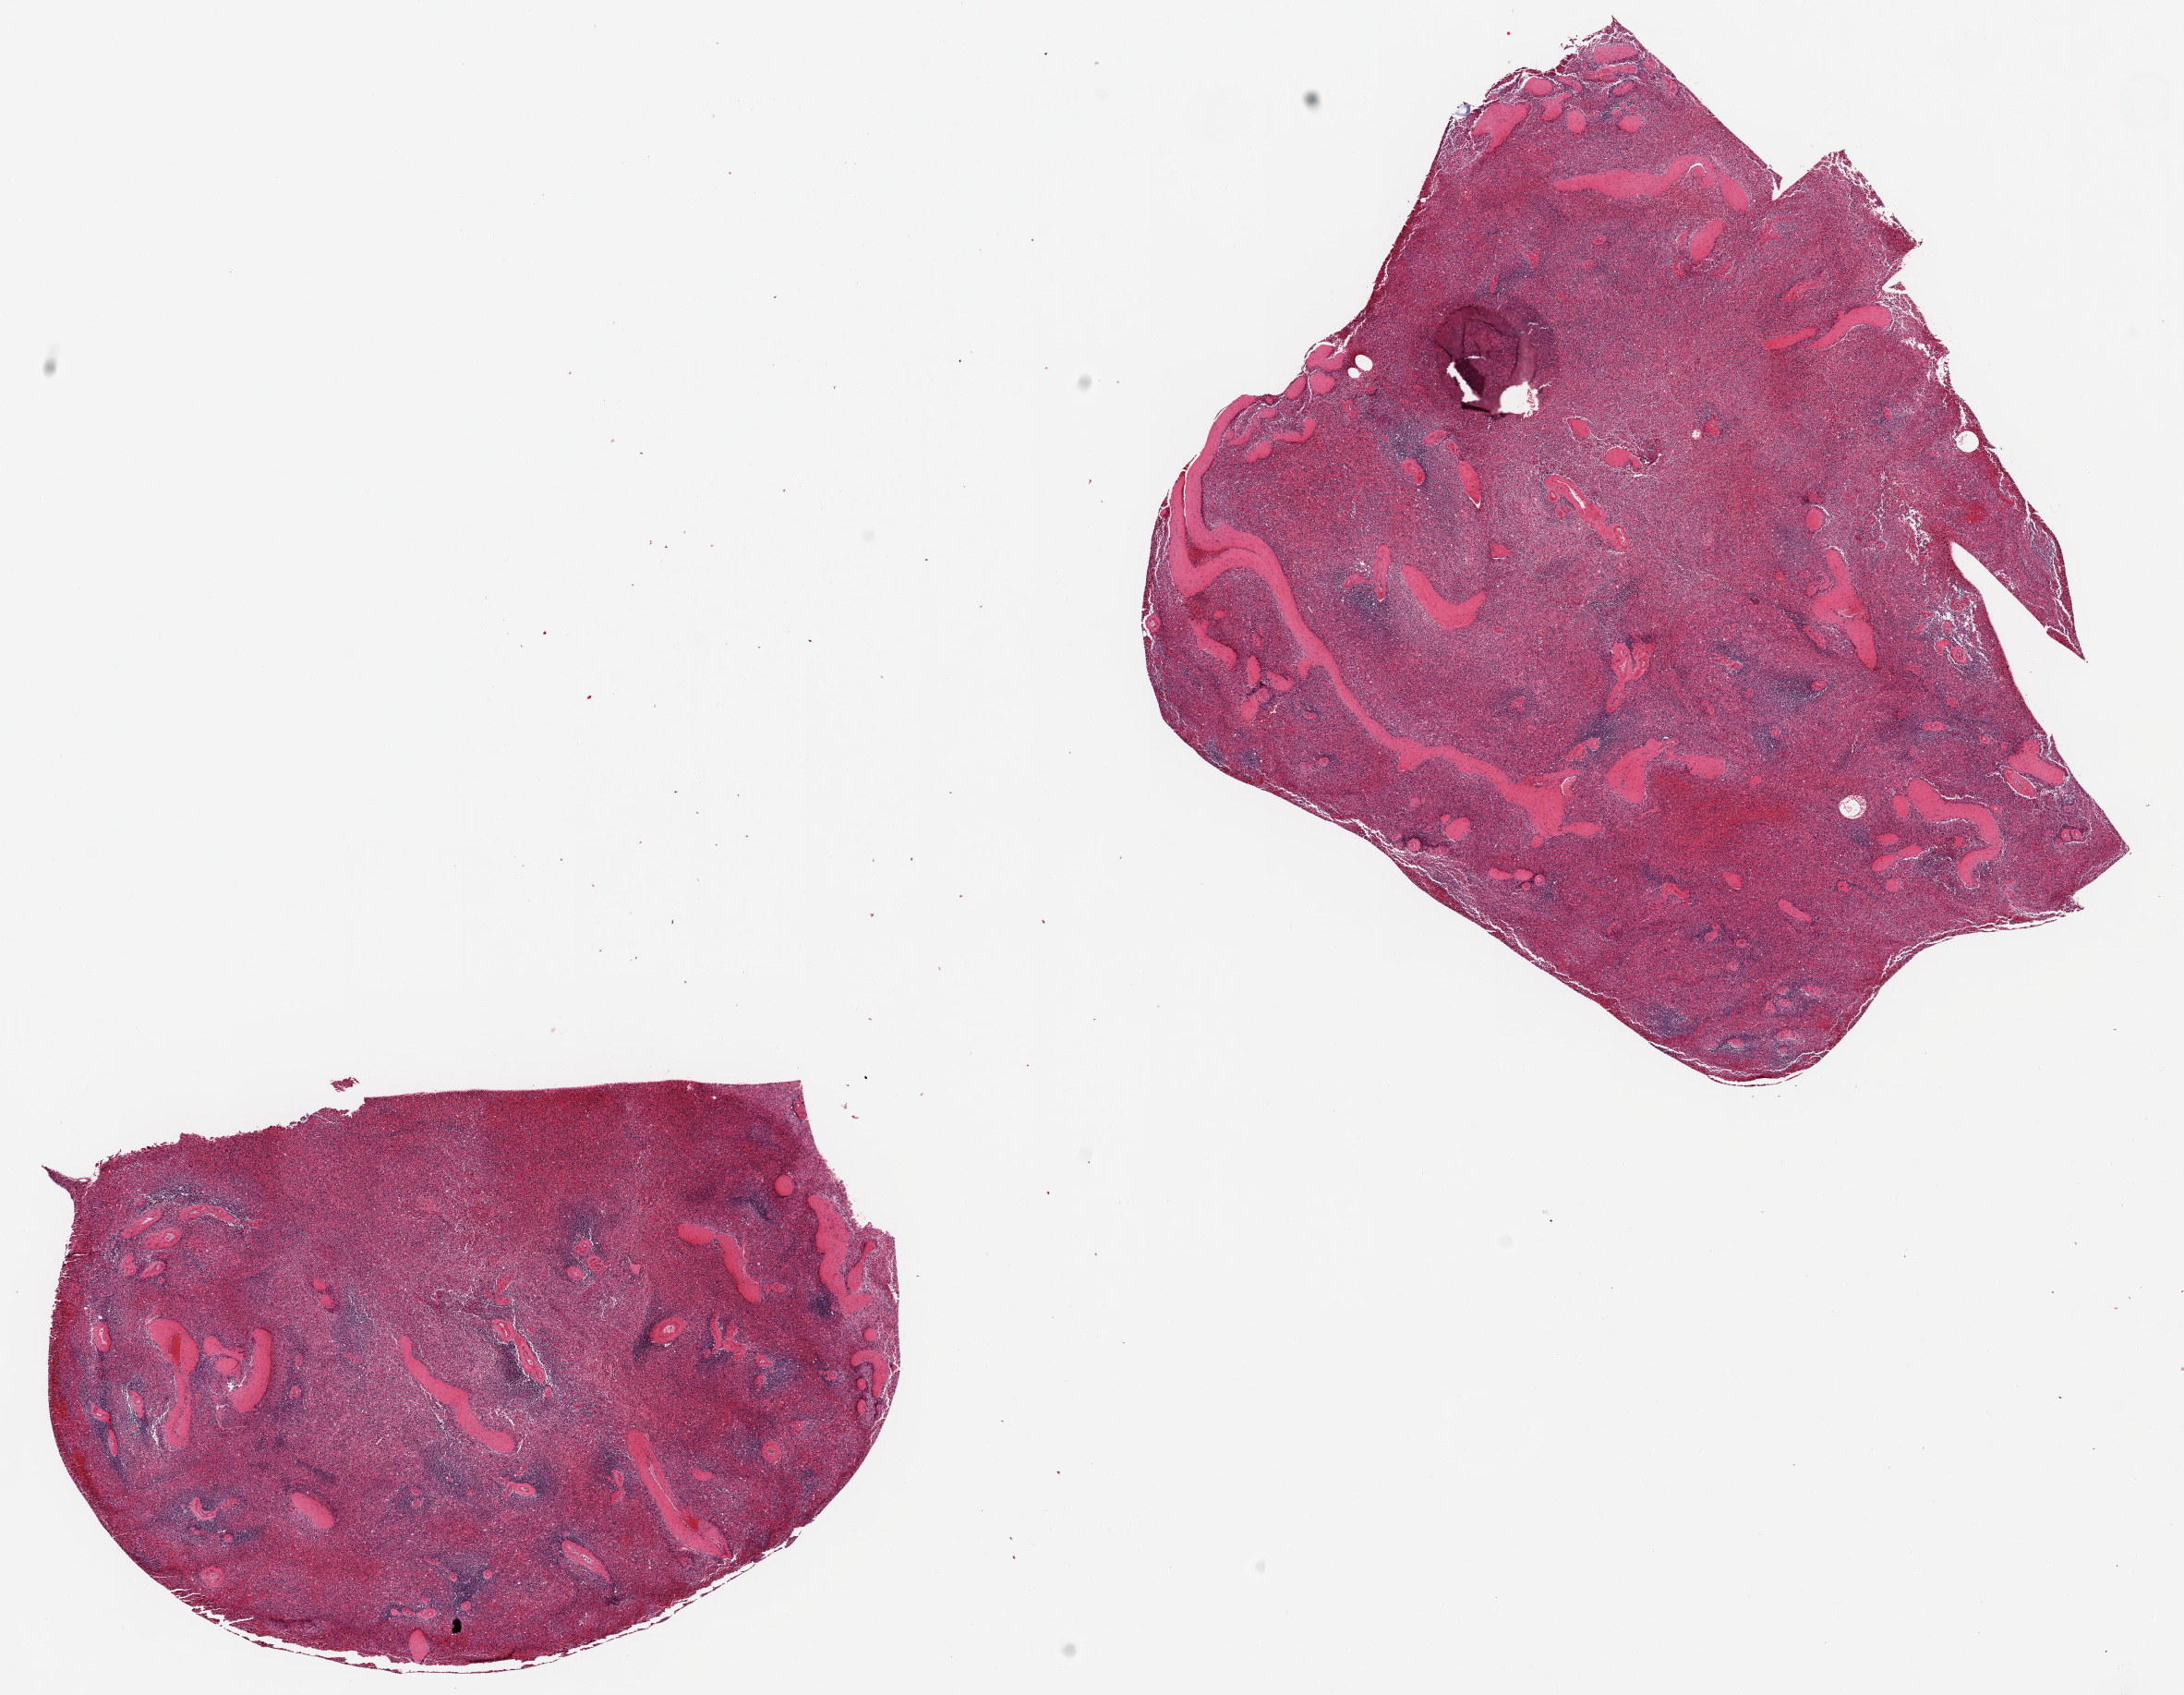
Whole-slide image, haematoxylin and eosin stain, brightfield — shown as a low-resolution overview of the whole scanned area (about 18.7 x 14.5 mm, acquisition: 20x scan); PAXgene-fixed, paraffin-embedded tissue; sampled site (target tissue): spleen; donor tissue sample. Female donor.
Review note (as recorded): 2 pieces. 7x5 & 9x7.5mm;congested.